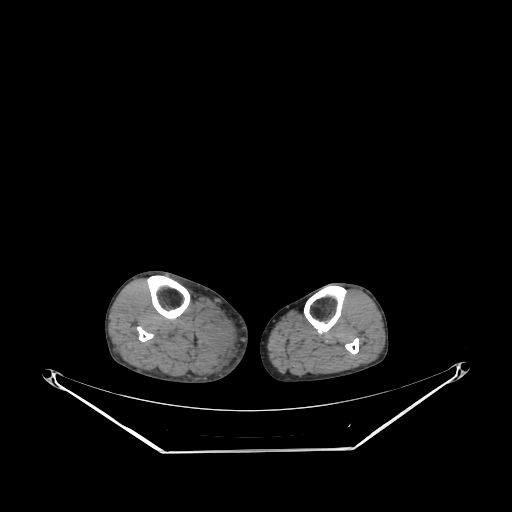
CT of an extremity soft-tissue mass (from a PET/CT study), one axial slice. Slice 146 of 267 in the series (ordered by position). Soft-tissue window (W 400 / L 40 HU). 512 × 512 image matrix, field of view 500 × 500 mm. Male patient. Case-level facts recorded for this patient, not image findings: histological type: pleiomorphic liposarcoma; grade: high; site of the primary tumour: right calf.
Structures marked on this image (expert contour drawn on MRI and transferred to this co-registered scan by the dataset authors):
- gross tumour volume including surrounding oedema: bounding box [x1, y1, x2, y2] px = [215, 315, 232, 353]